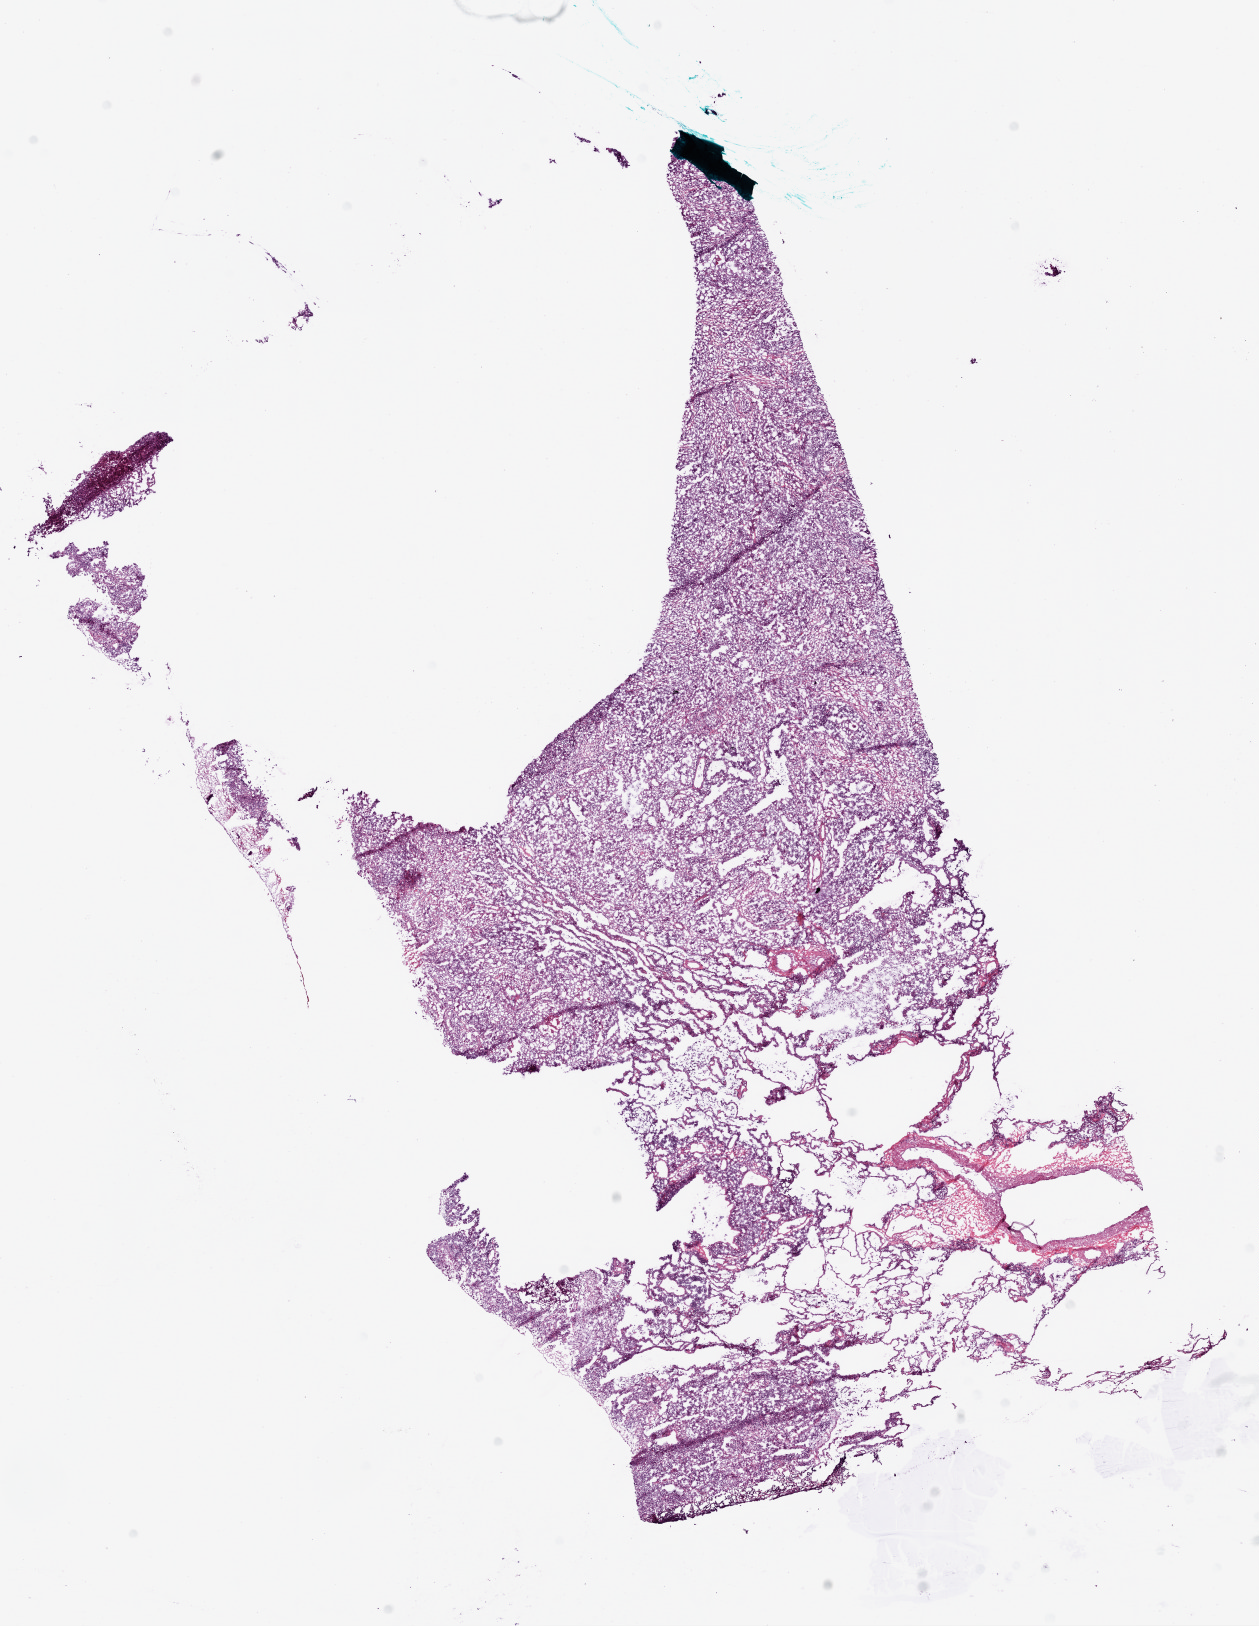
Whole-slide histology image, H&E, low-resolution overview of the scanned area, about 10.2 x 13.1 mm (acquisition: 20x scan), frozen section from the bottom of the tissue portion, primary tumour sample from the lung. Patient: male, age at initial diagnosis 63 years. Slide review estimates, as recorded: tumour nuclei 60%, necrosis 3%.
TNM: T1 N0 M0. AJCC pathologic stage: IA. Diagnosis: Squamous cell carcinoma, NOS. Laterality: right.